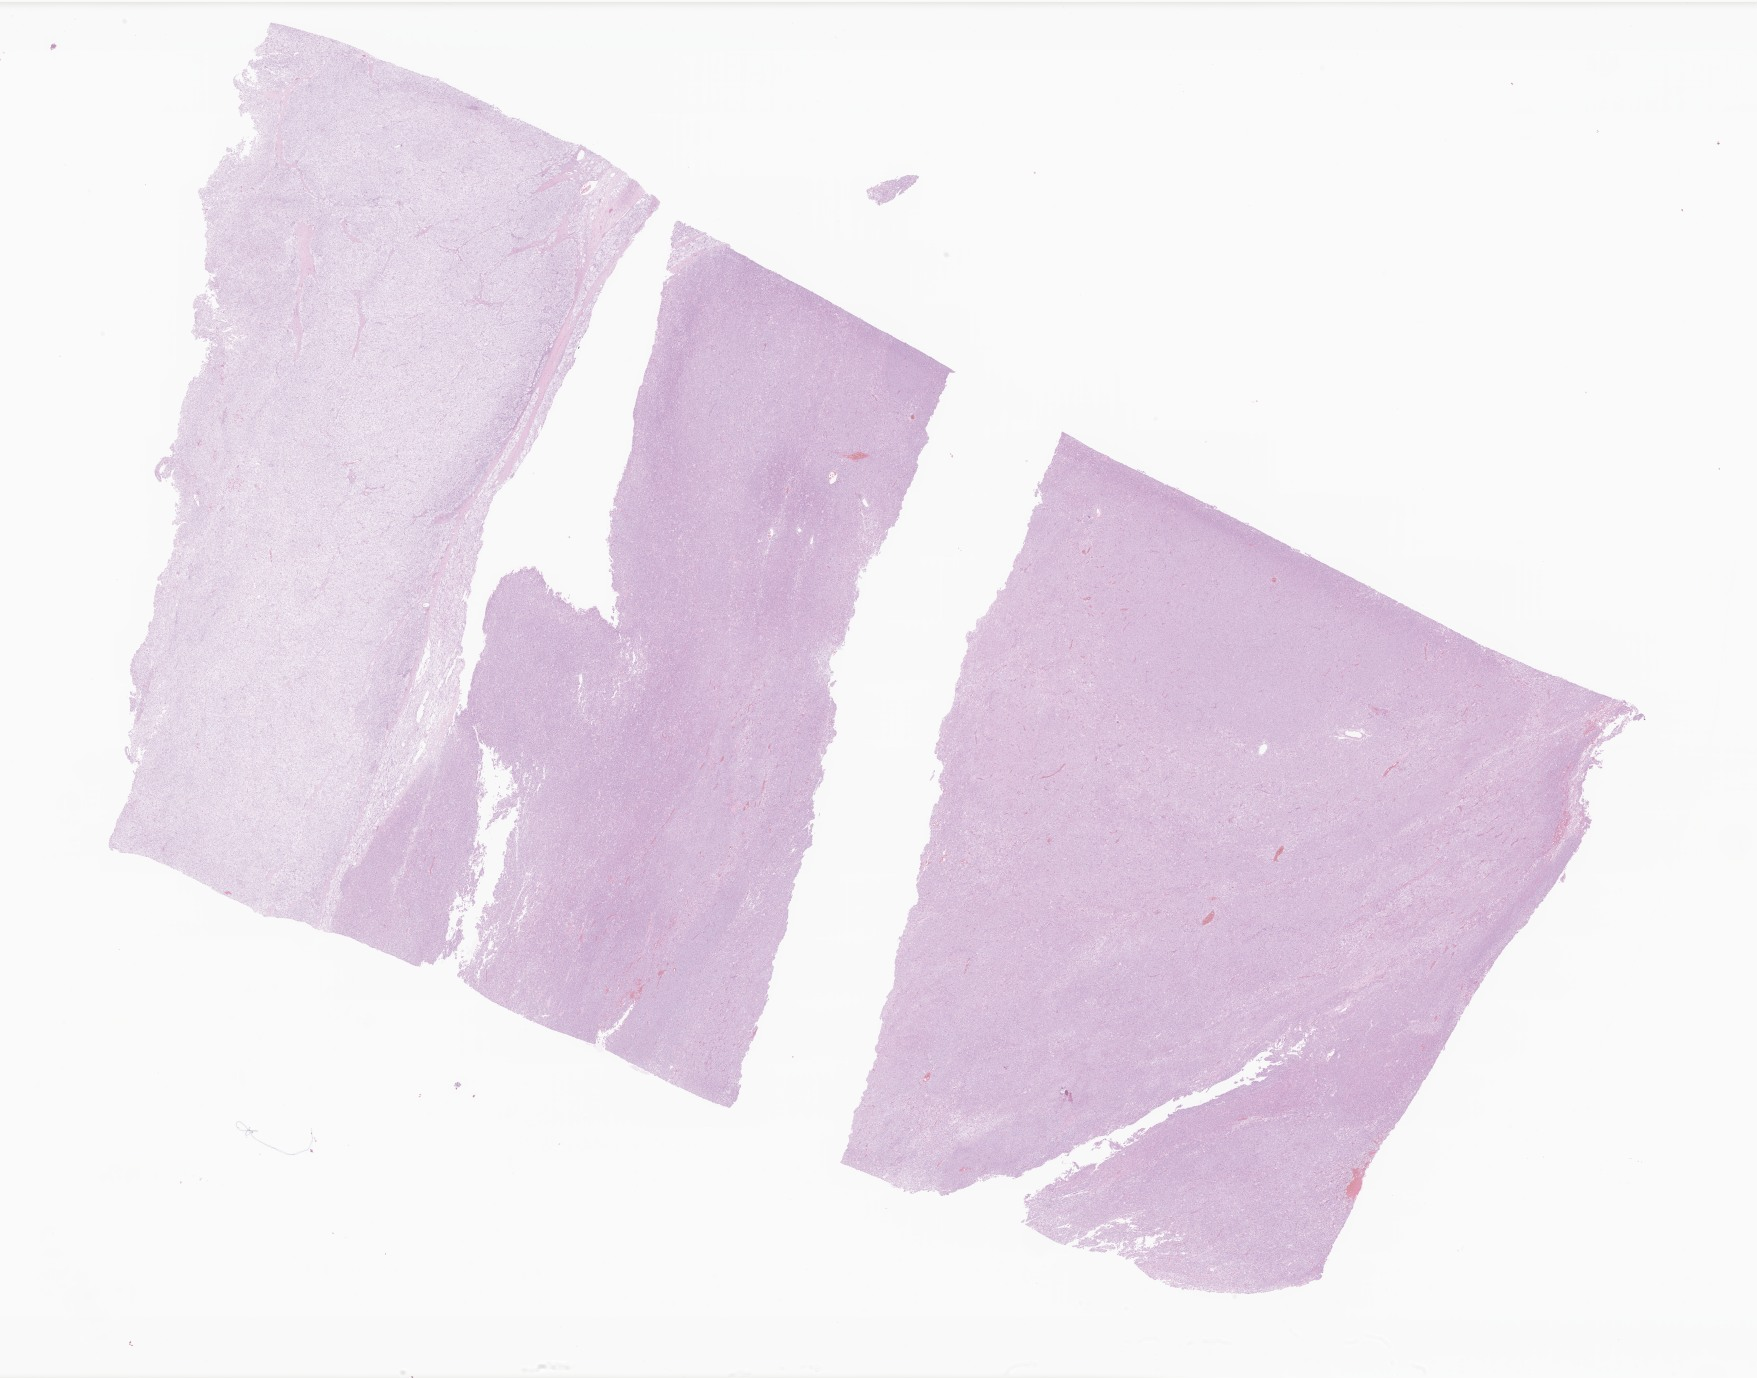
Whole-slide image, hematoxylin and eosin (H&E) stain of tumor tissue from the pelvis, shown as a low-resolution overview of the whole scanned area (about 29.6 x 23.2 mm). Formalin-fixed paraffin-embedded section. Patient: female, age 156 months (13 years).
* diagnosis (ICD-O-3 morphology term): Neoplasm, uncertain whether benign or malignant